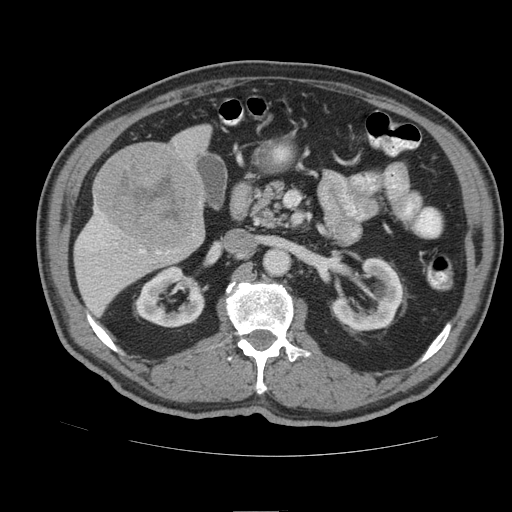
Contrast-enhanced abdominal CT (liver protocol), one axial slice; slice 39 of 105 in the series (ordered by position); soft-tissue window (W 400 / L 40 HU); 512 × 512 image matrix, field of view 380 × 380 mm. Case-level facts recorded for this patient, not image findings: diagnosis: hepatocellular carcinoma (patient treated with transarterial chemoembolisation; whether this scan precedes or follows treatment is not stated here); TNM stage (as recorded): Stage-IIIB; Child-Pugh class: A; tumour nodularity: multinodular.
Annotated regions visible in this slice (semi-automatically segmented with operator editing):
- liver parenchyma outside the tumour (the mass and vessels are separate outlines, so this box may not span the whole liver): bounding box (x1, y1, x2, y2) in pixels: (74, 124, 212, 316)
- mass: (94, 145, 203, 250)
- liver vessels: (83, 220, 160, 254)